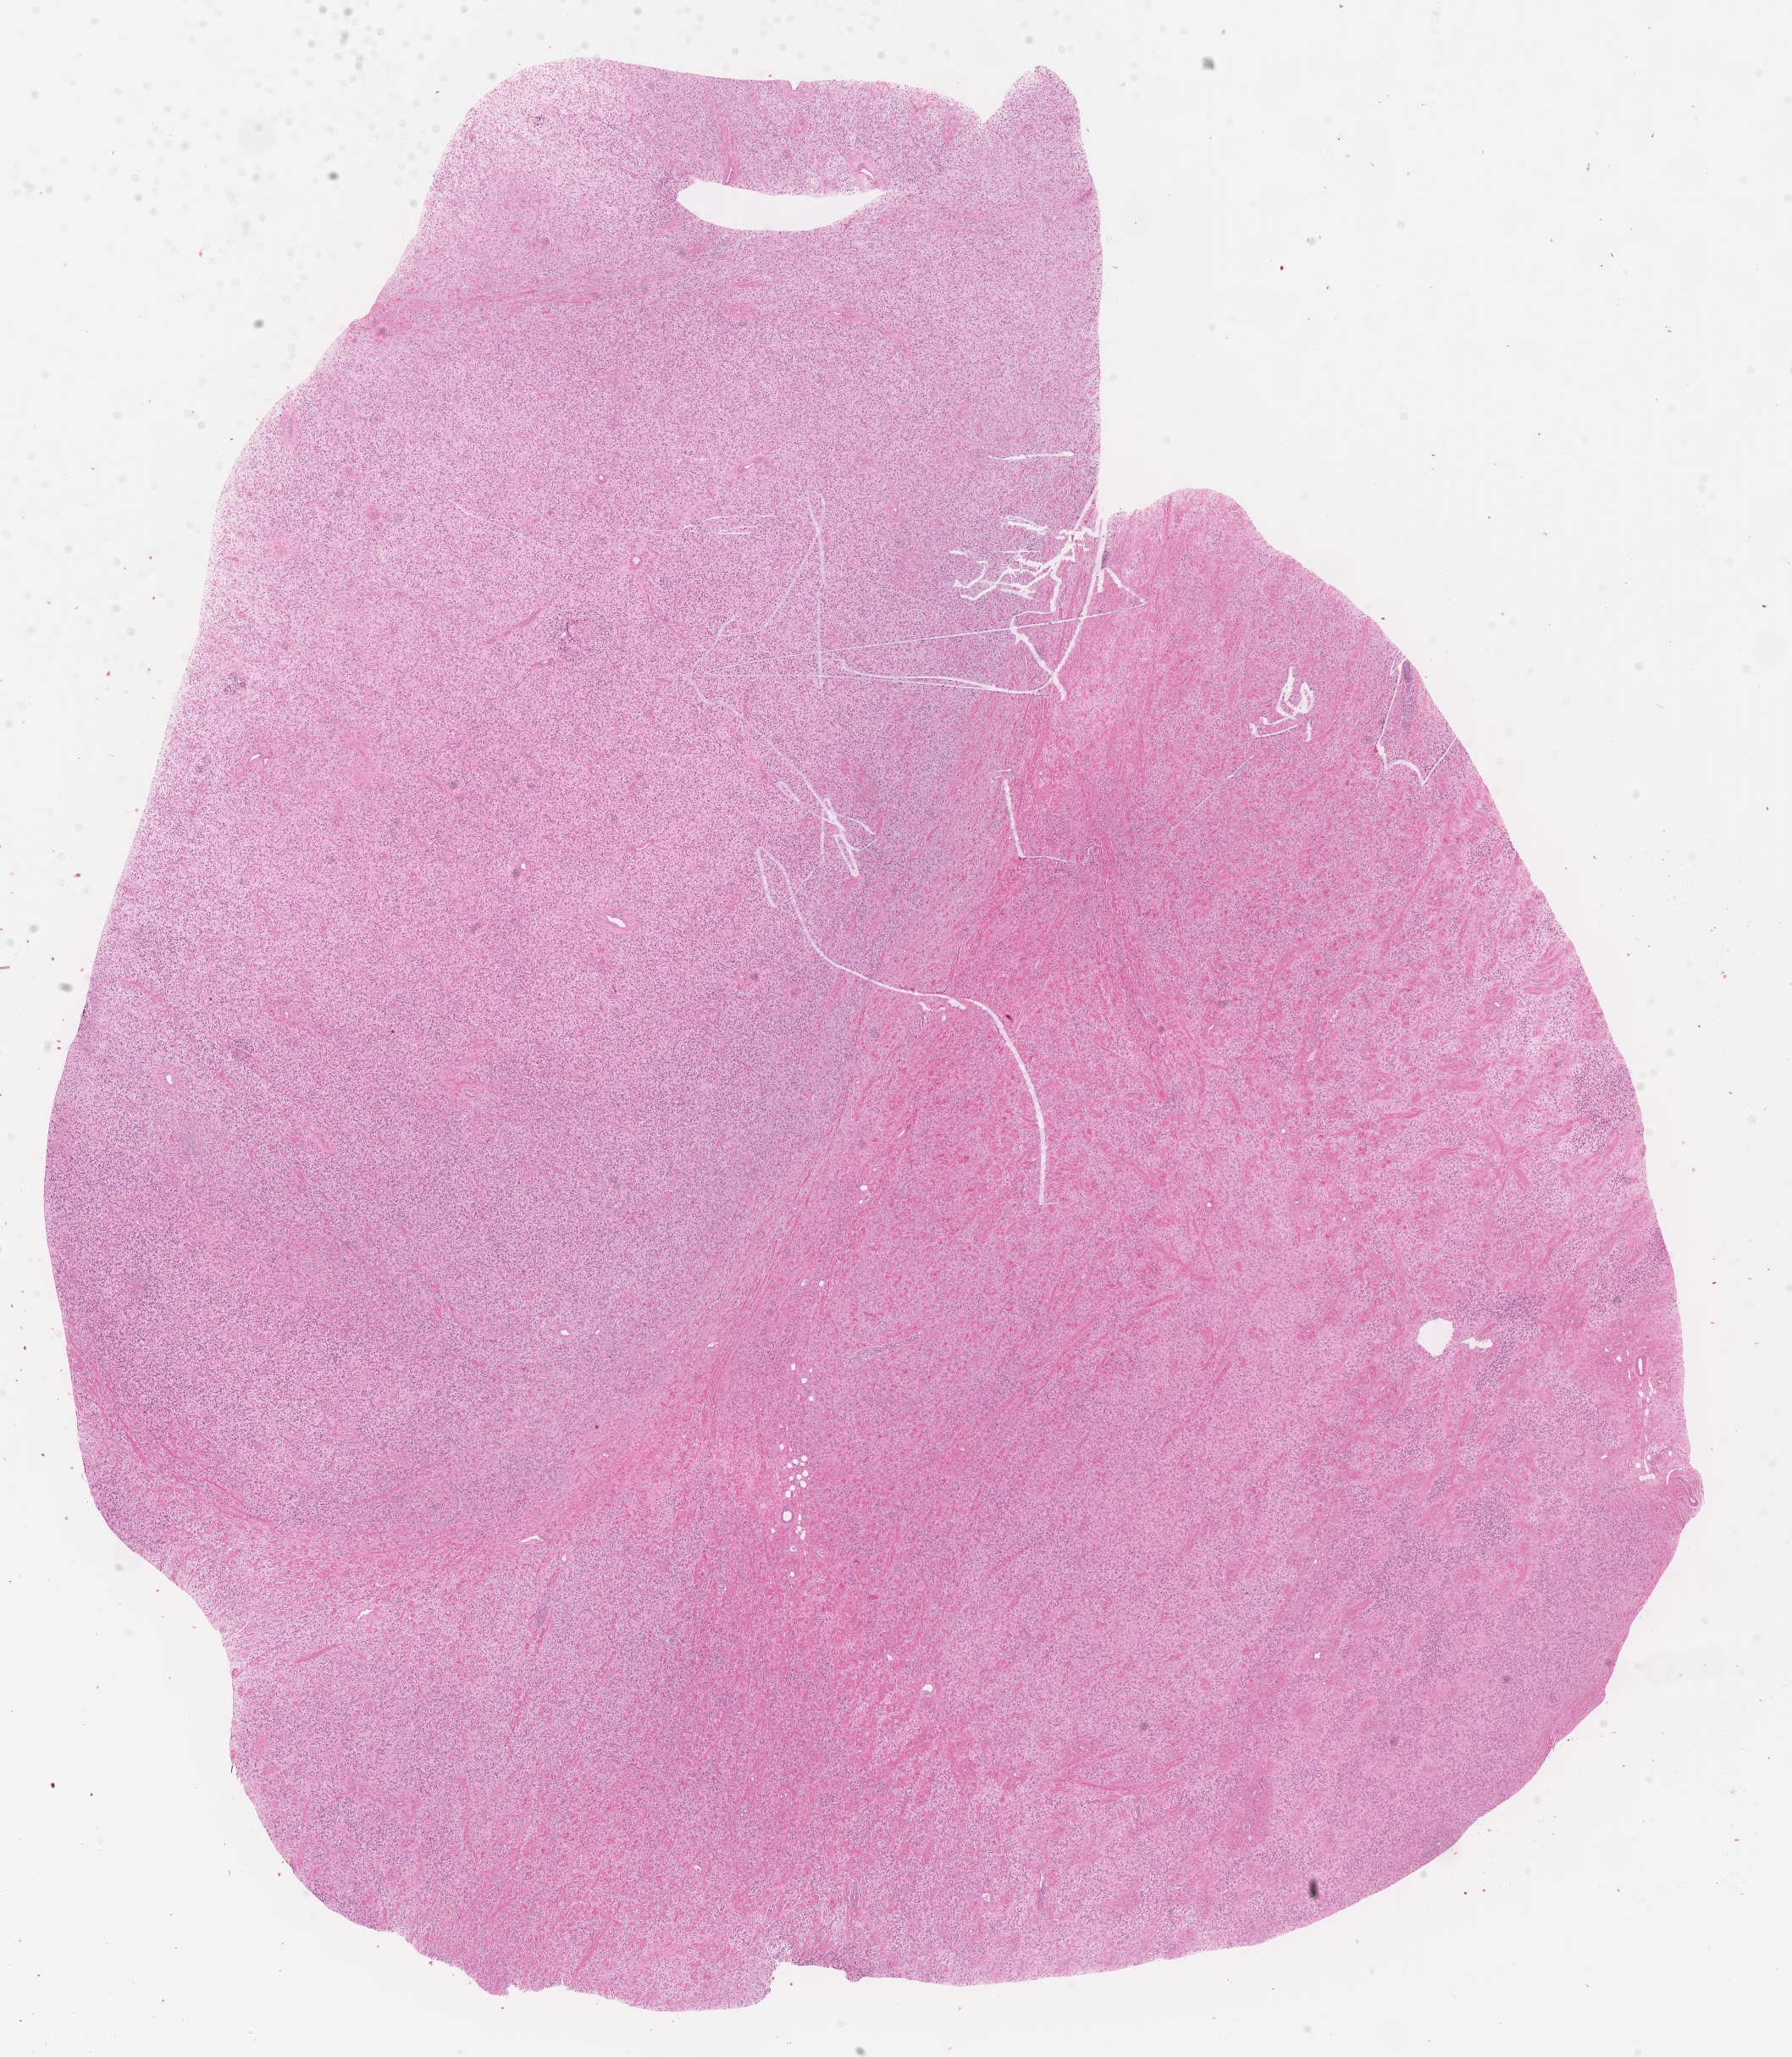
H&E whole-slide image of tumor tissue — shown as a low-resolution overview of the whole scanned area (about 17.1 x 19.6 mm), formalin-fixed paraffin-embedded section, site: testicle-right. Patient: male, age 10.9 years at diagnosis.
Metastatic status at presentation (as recorded): non-metastatic. Stage (as recorded): 1. Diagnosis: rhabdomyosarcoma; histological classification: embryonal rhabdomyosarcoma.